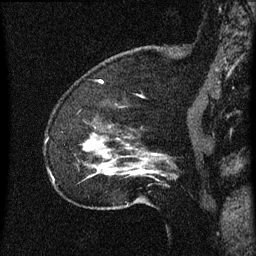
Breast MRI (dynamic contrast-enhanced), one sagittal slice. Position 13 of 60 along the scan axis. Dynamic contrast-enhanced series, image 2 of 3 at this slice position (ordered by acquisition). 1.5 T. TE 4.2 ms, TR 8 ms. 2 mm slice thickness. 256 × 256 image matrix, field of view 180 × 180 mm. Patient: female, 52 years.
Structures marked on this image (semi-automatically segmented with operator editing):
- analysis volume of interest (the breast-tissue region the enhancement analysis was run in; not a lesion): bounding box <54,120,169,207> (left, top, right, bottom; pixels)
- tumour enhancement mask (voxels above the 70 % enhancement threshold inside the analysis volume of interest): <87,140,157,175>